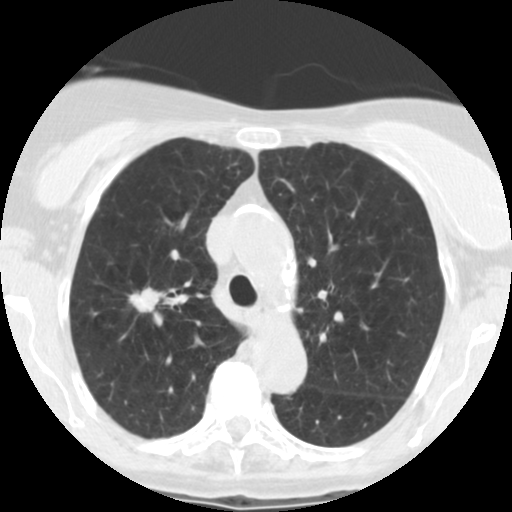
Low-dose screening chest CT, one axial slice; reconstruction kernel STANDARD; 120 kVp; lung window (W 1500 / L -600 HU); 512 × 512 image matrix.
Structures marked on this image (outlined manually by an expert reader):
- lesion 1 (tumor, upper lobe of right lung): bounding box [x1, y1, x2, y2] px = [129, 287, 164, 313]